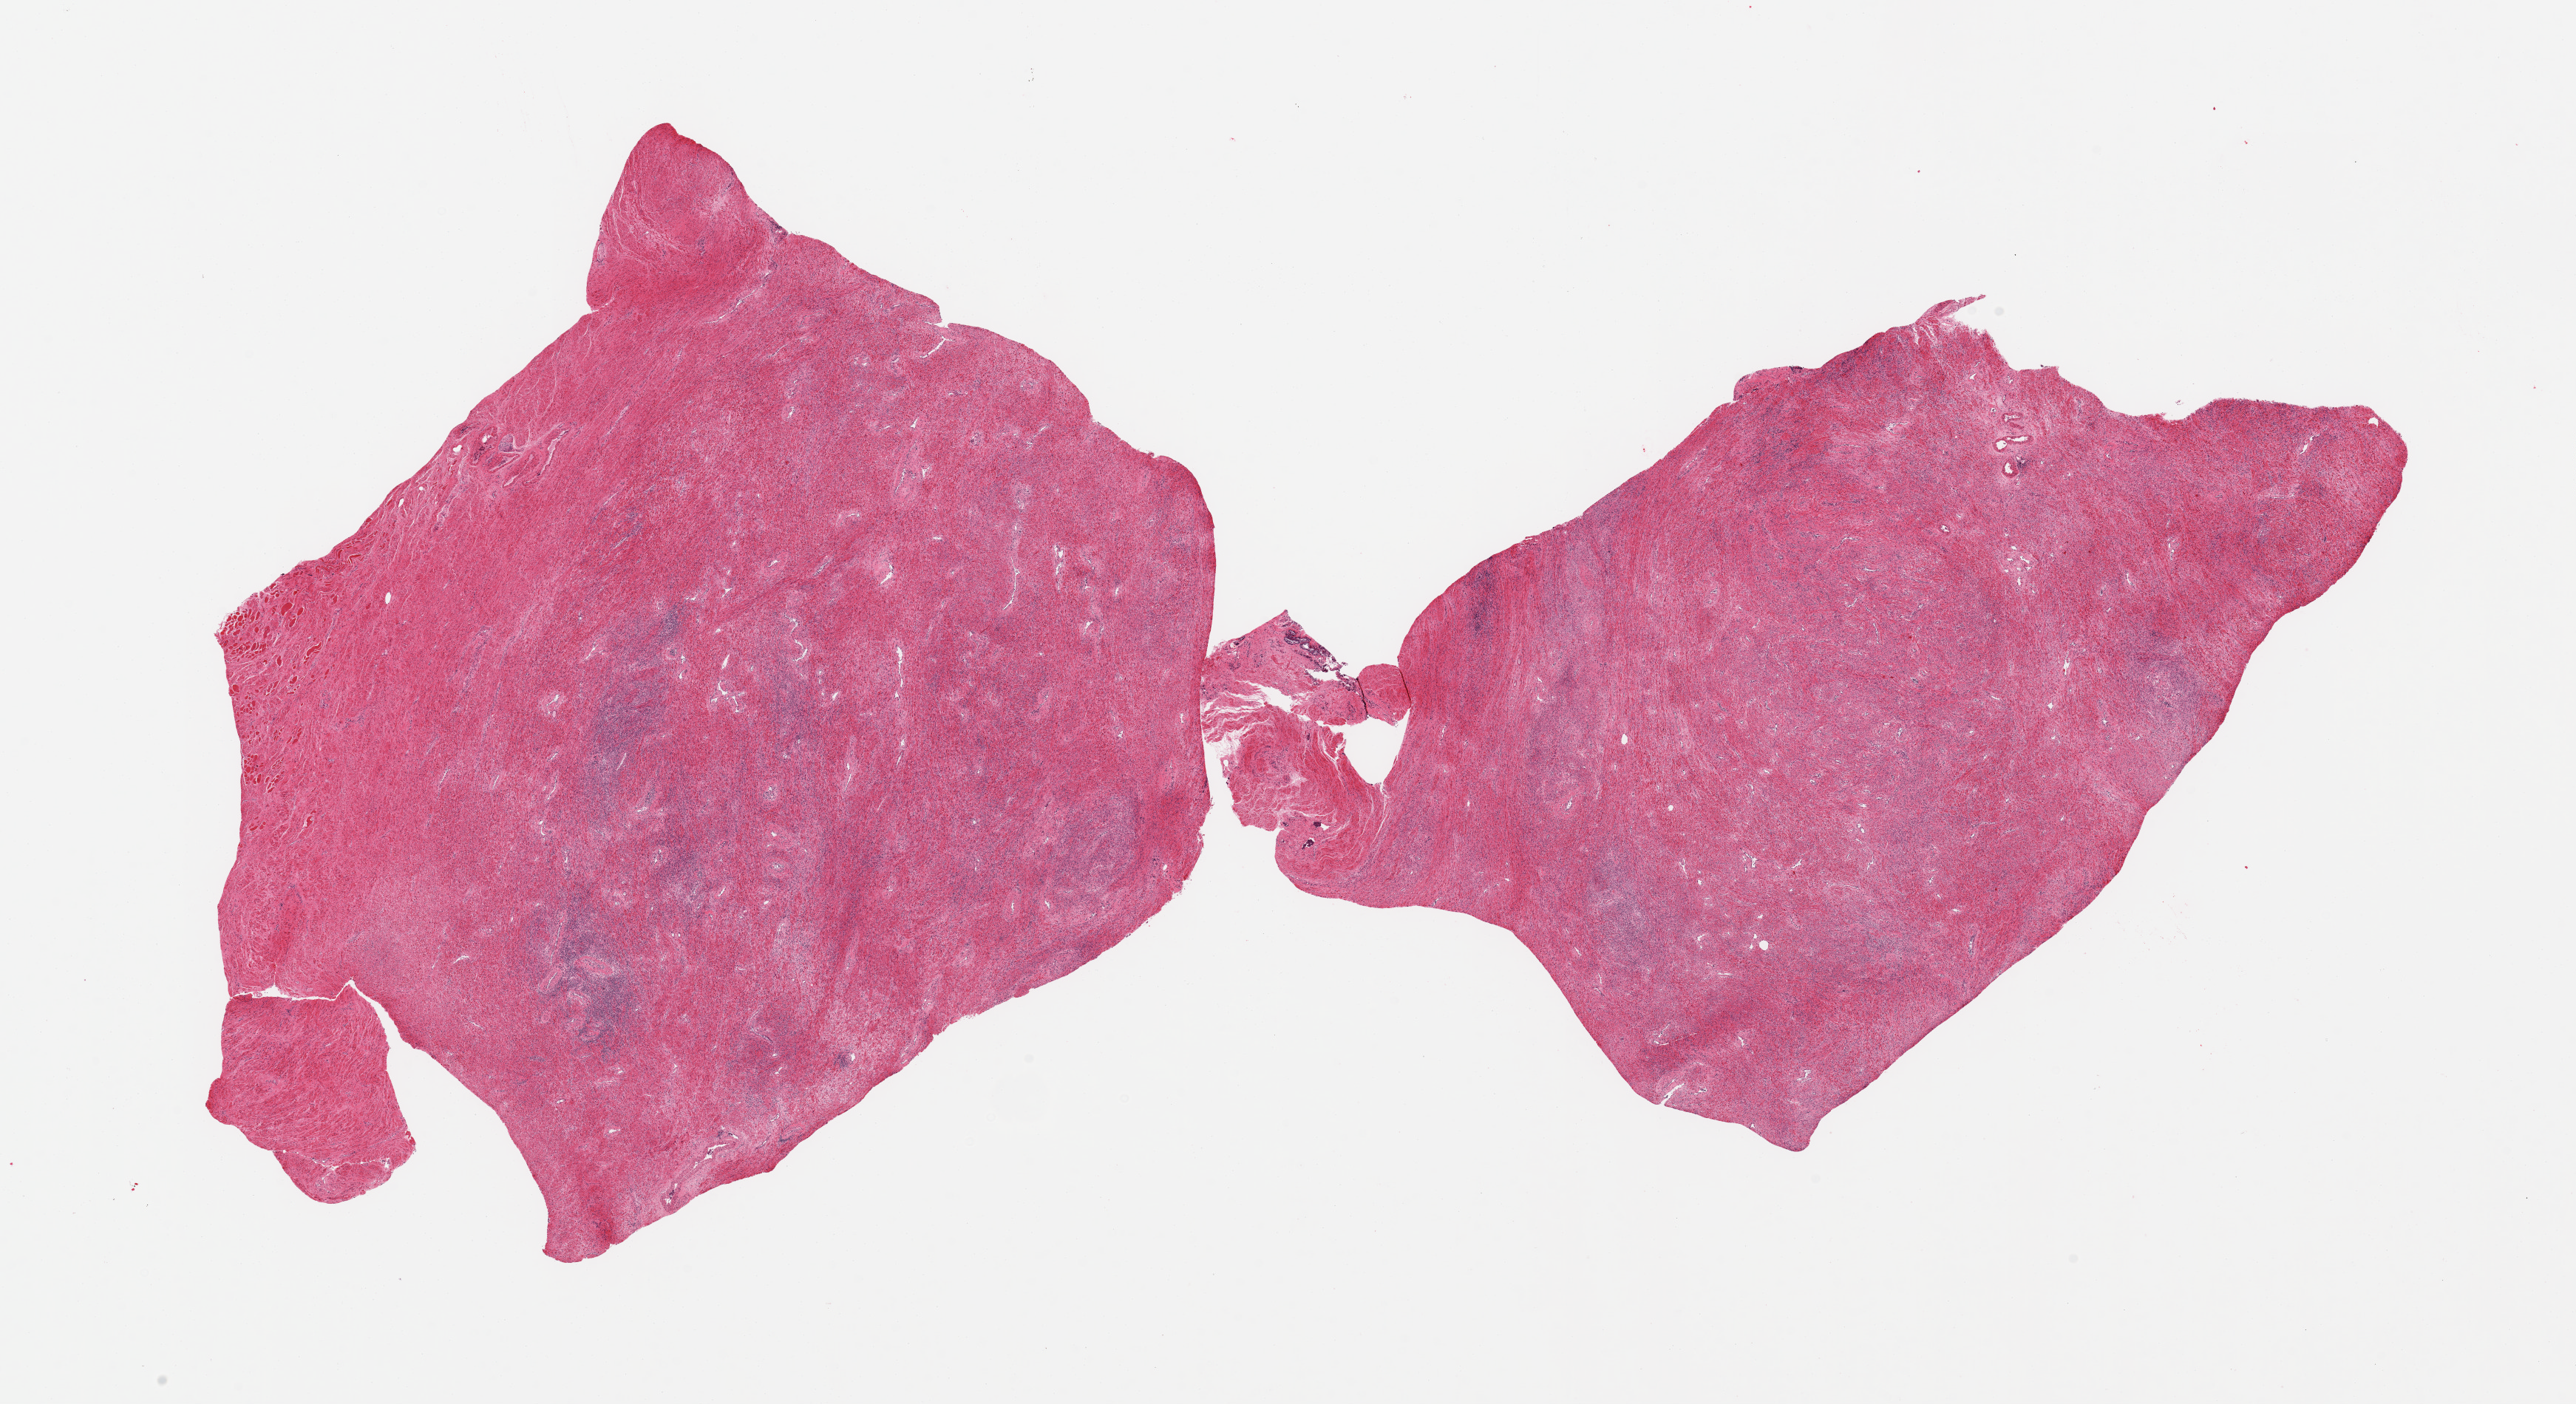
Digitized hematoxylin and eosin (H&E)-stained section, a low-resolution overview of the entire scanned area, about 27.6 x 15.0 mm; PAXgene-fixed paraffin-embedded (PFPE) section; section of prostate (target tissue); donor tissue sample. Donor: male.
• review note (as recorded): 2 pieces, stromal elements only, patchy chronic prostatitis